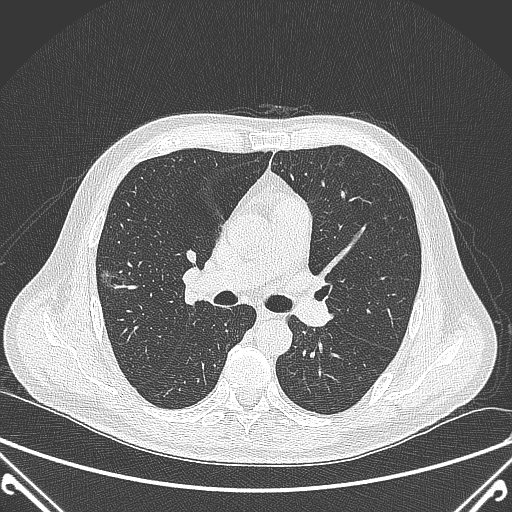
Chest CT, one axial slice; position 221 of 360 along the scan axis; lung window (W 1500 / L -600 HU); 512 × 512 image matrix, field of view 380 × 380 mm. Patient: male, 64 years. From the clinical record (not read from this slice): clinical TNM (as recorded): T1c N0 M0.
Annotated regions visible in this slice (rectangle marked by the reading radiologist):
- lung tumour (recorded histology: adenocarcinoma): bounding box [x1, y1, x2, y2] px = [93, 262, 128, 290]